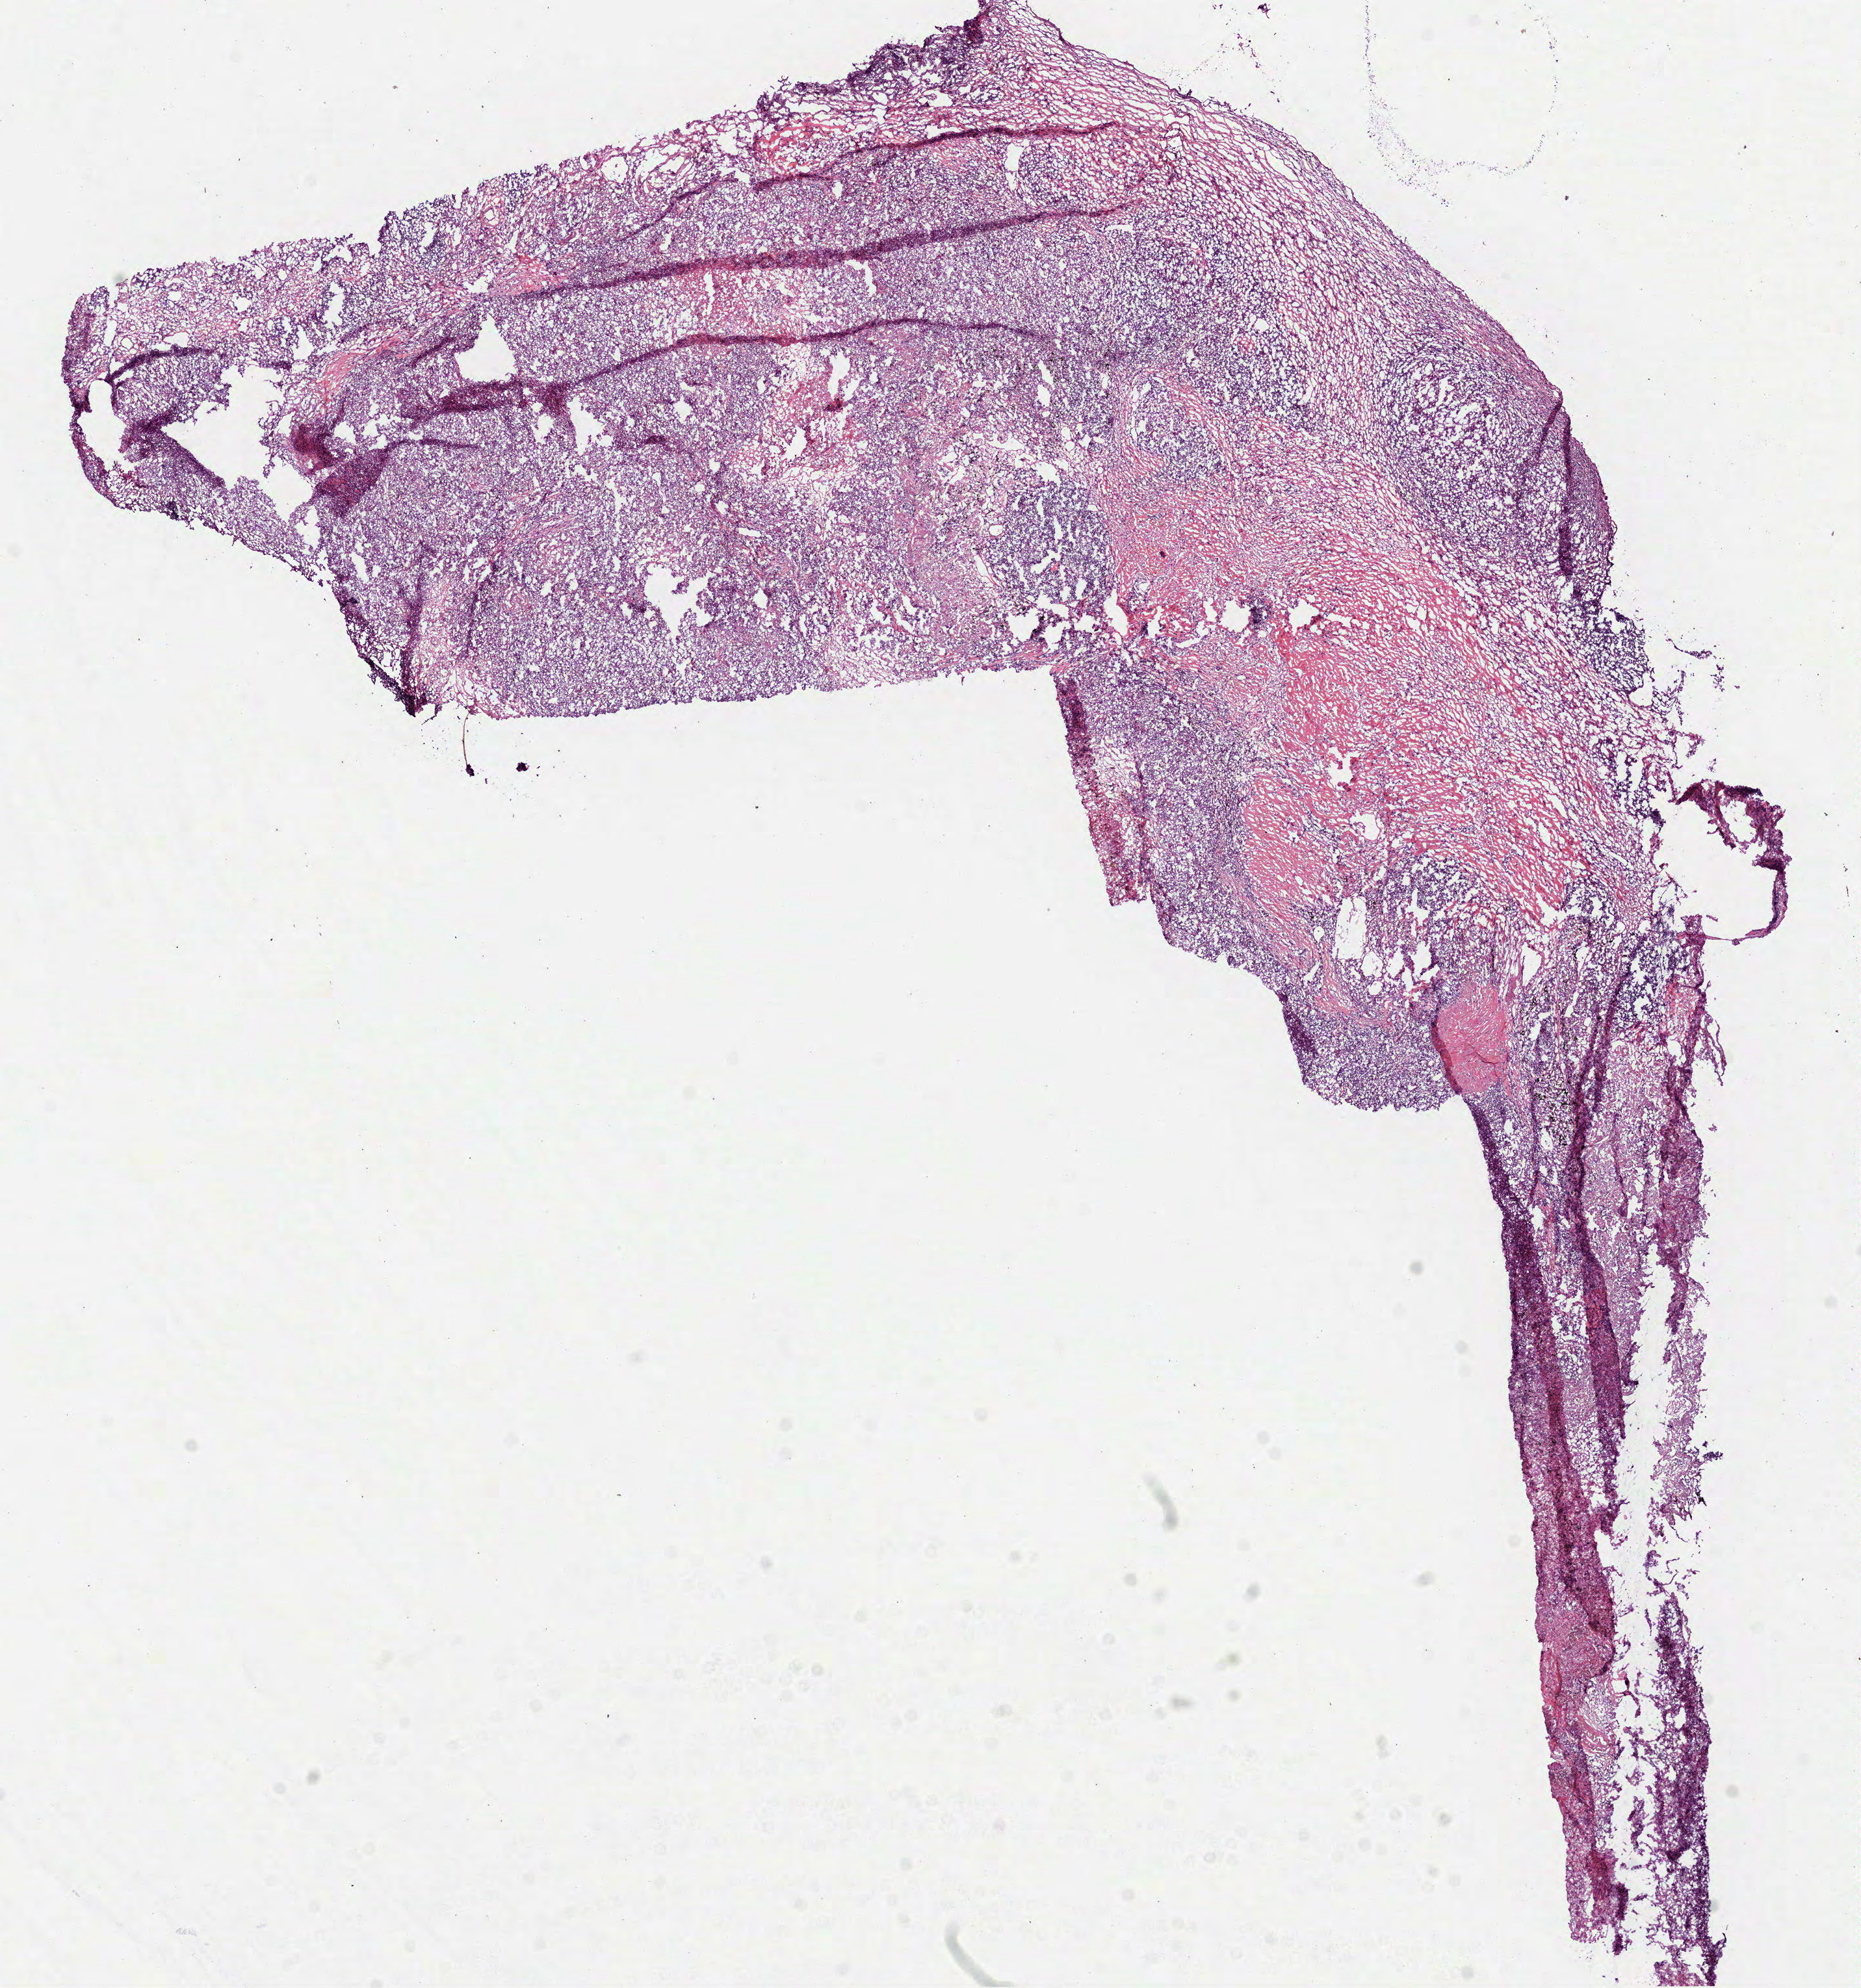
Digitized H&E-stained tissue section (whole slide), low-resolution overview of the scanned area, about 11.5 x 12.3 mm, frozen section from the bottom of the tissue portion, lung, primary tumour sample. Female patient; age at initial diagnosis 72 years. Slide review estimates, as recorded: tumour cells 75%, tumour nuclei 68%, normal cells 0%, stromal cells 25%, necrosis 0%.
- laterality: right
- diagnosis: Adenocarcinoma, NOS
- AJCC pathologic stage: IB (6th edition)